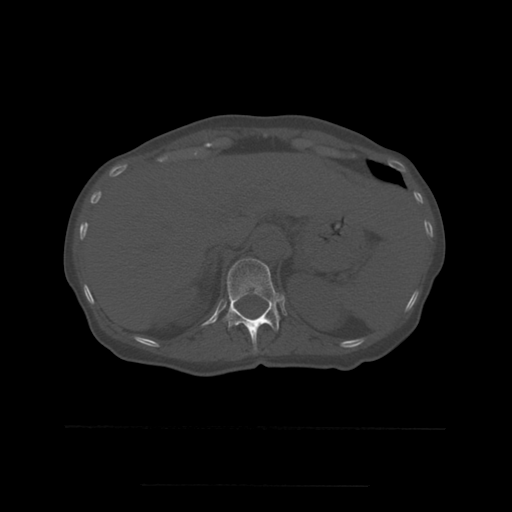
CT including the spine, one axial slice; slice 259 of 544 in the series (ordered by position); bone window (W 1800 / L 400 HU); 1.25 mm slice thickness; 512 × 512 image matrix, field of view 350 × 350 mm. Patient age 58 years. From the clinical record (not read from this slice): primary cancer: lung.
Outlined on this slice (semi-automatically segmented with operator editing):
- T12 vertebra: bounding box [x1, y1, x2, y2] px = [224, 259, 280, 351]